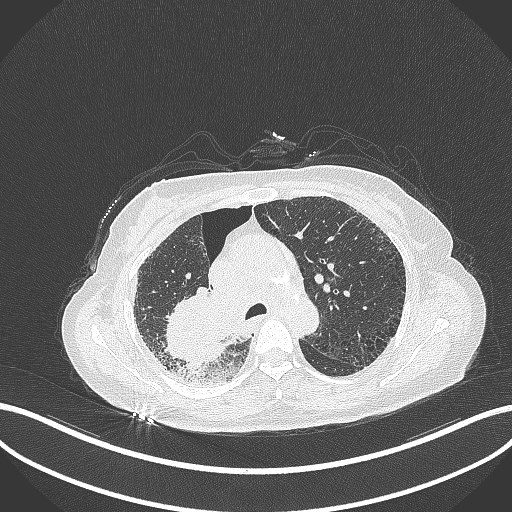
Chest CT, one axial slice; position 233 of 408 along the scan axis; reconstruction kernel B70f; lung window (W 1500 / L -600 HU); 512 × 512 image matrix, field of view 400 × 400 mm. Female patient, age 64 years. From the clinical record (not read from this slice): clinical TNM (as recorded): T3 N3 M0.
Structures marked on this image (rectangle marked by the reading radiologist):
- lung tumour (recorded histology: squamous cell carcinoma): bounding box (x1, y1, x2, y2) in pixels: (162, 288, 232, 371)